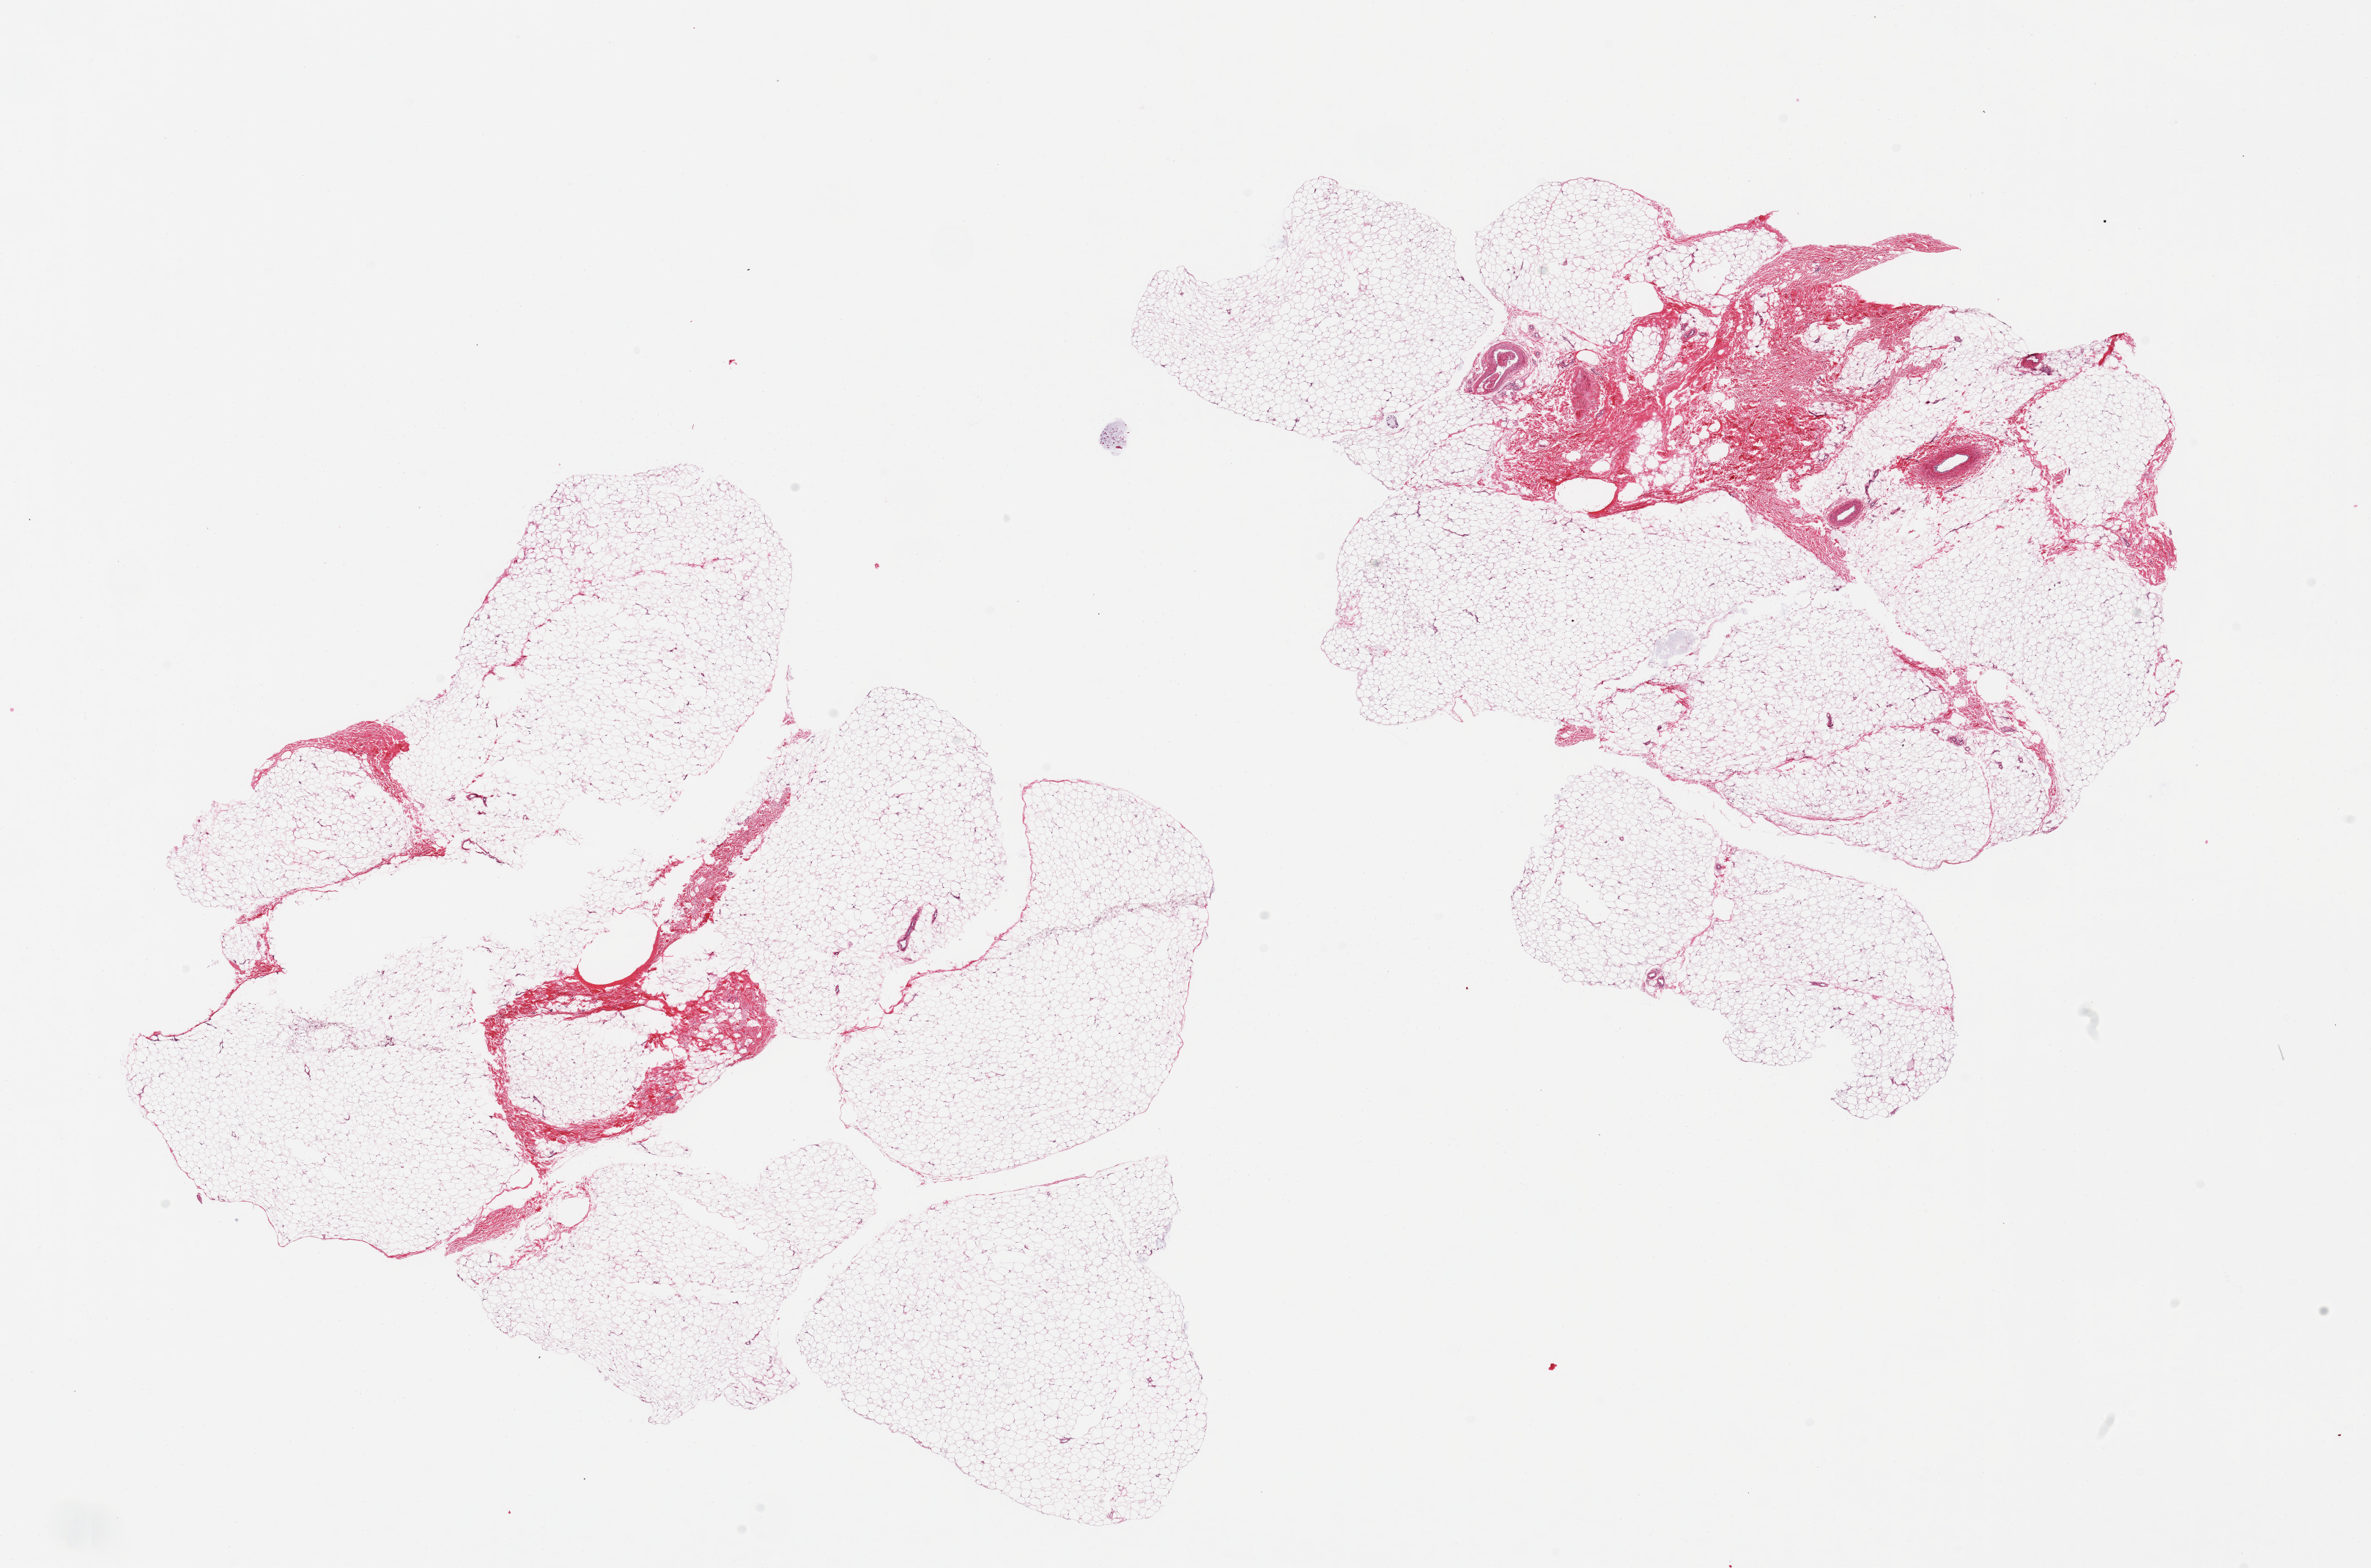
Digitized hematoxylin and eosin (H&E)-stained section — low-resolution overview of the scanned area, about 25.6 x 16.9 mm; PAXgene-fixed, paraffin-embedded tissue; sampled site (target tissue): breast; tissue donor sample. Donor: male.
Review note (as recorded): 2 pieces; 80 and 90% fat with small portion of fibrous tissue, no ductal elements.